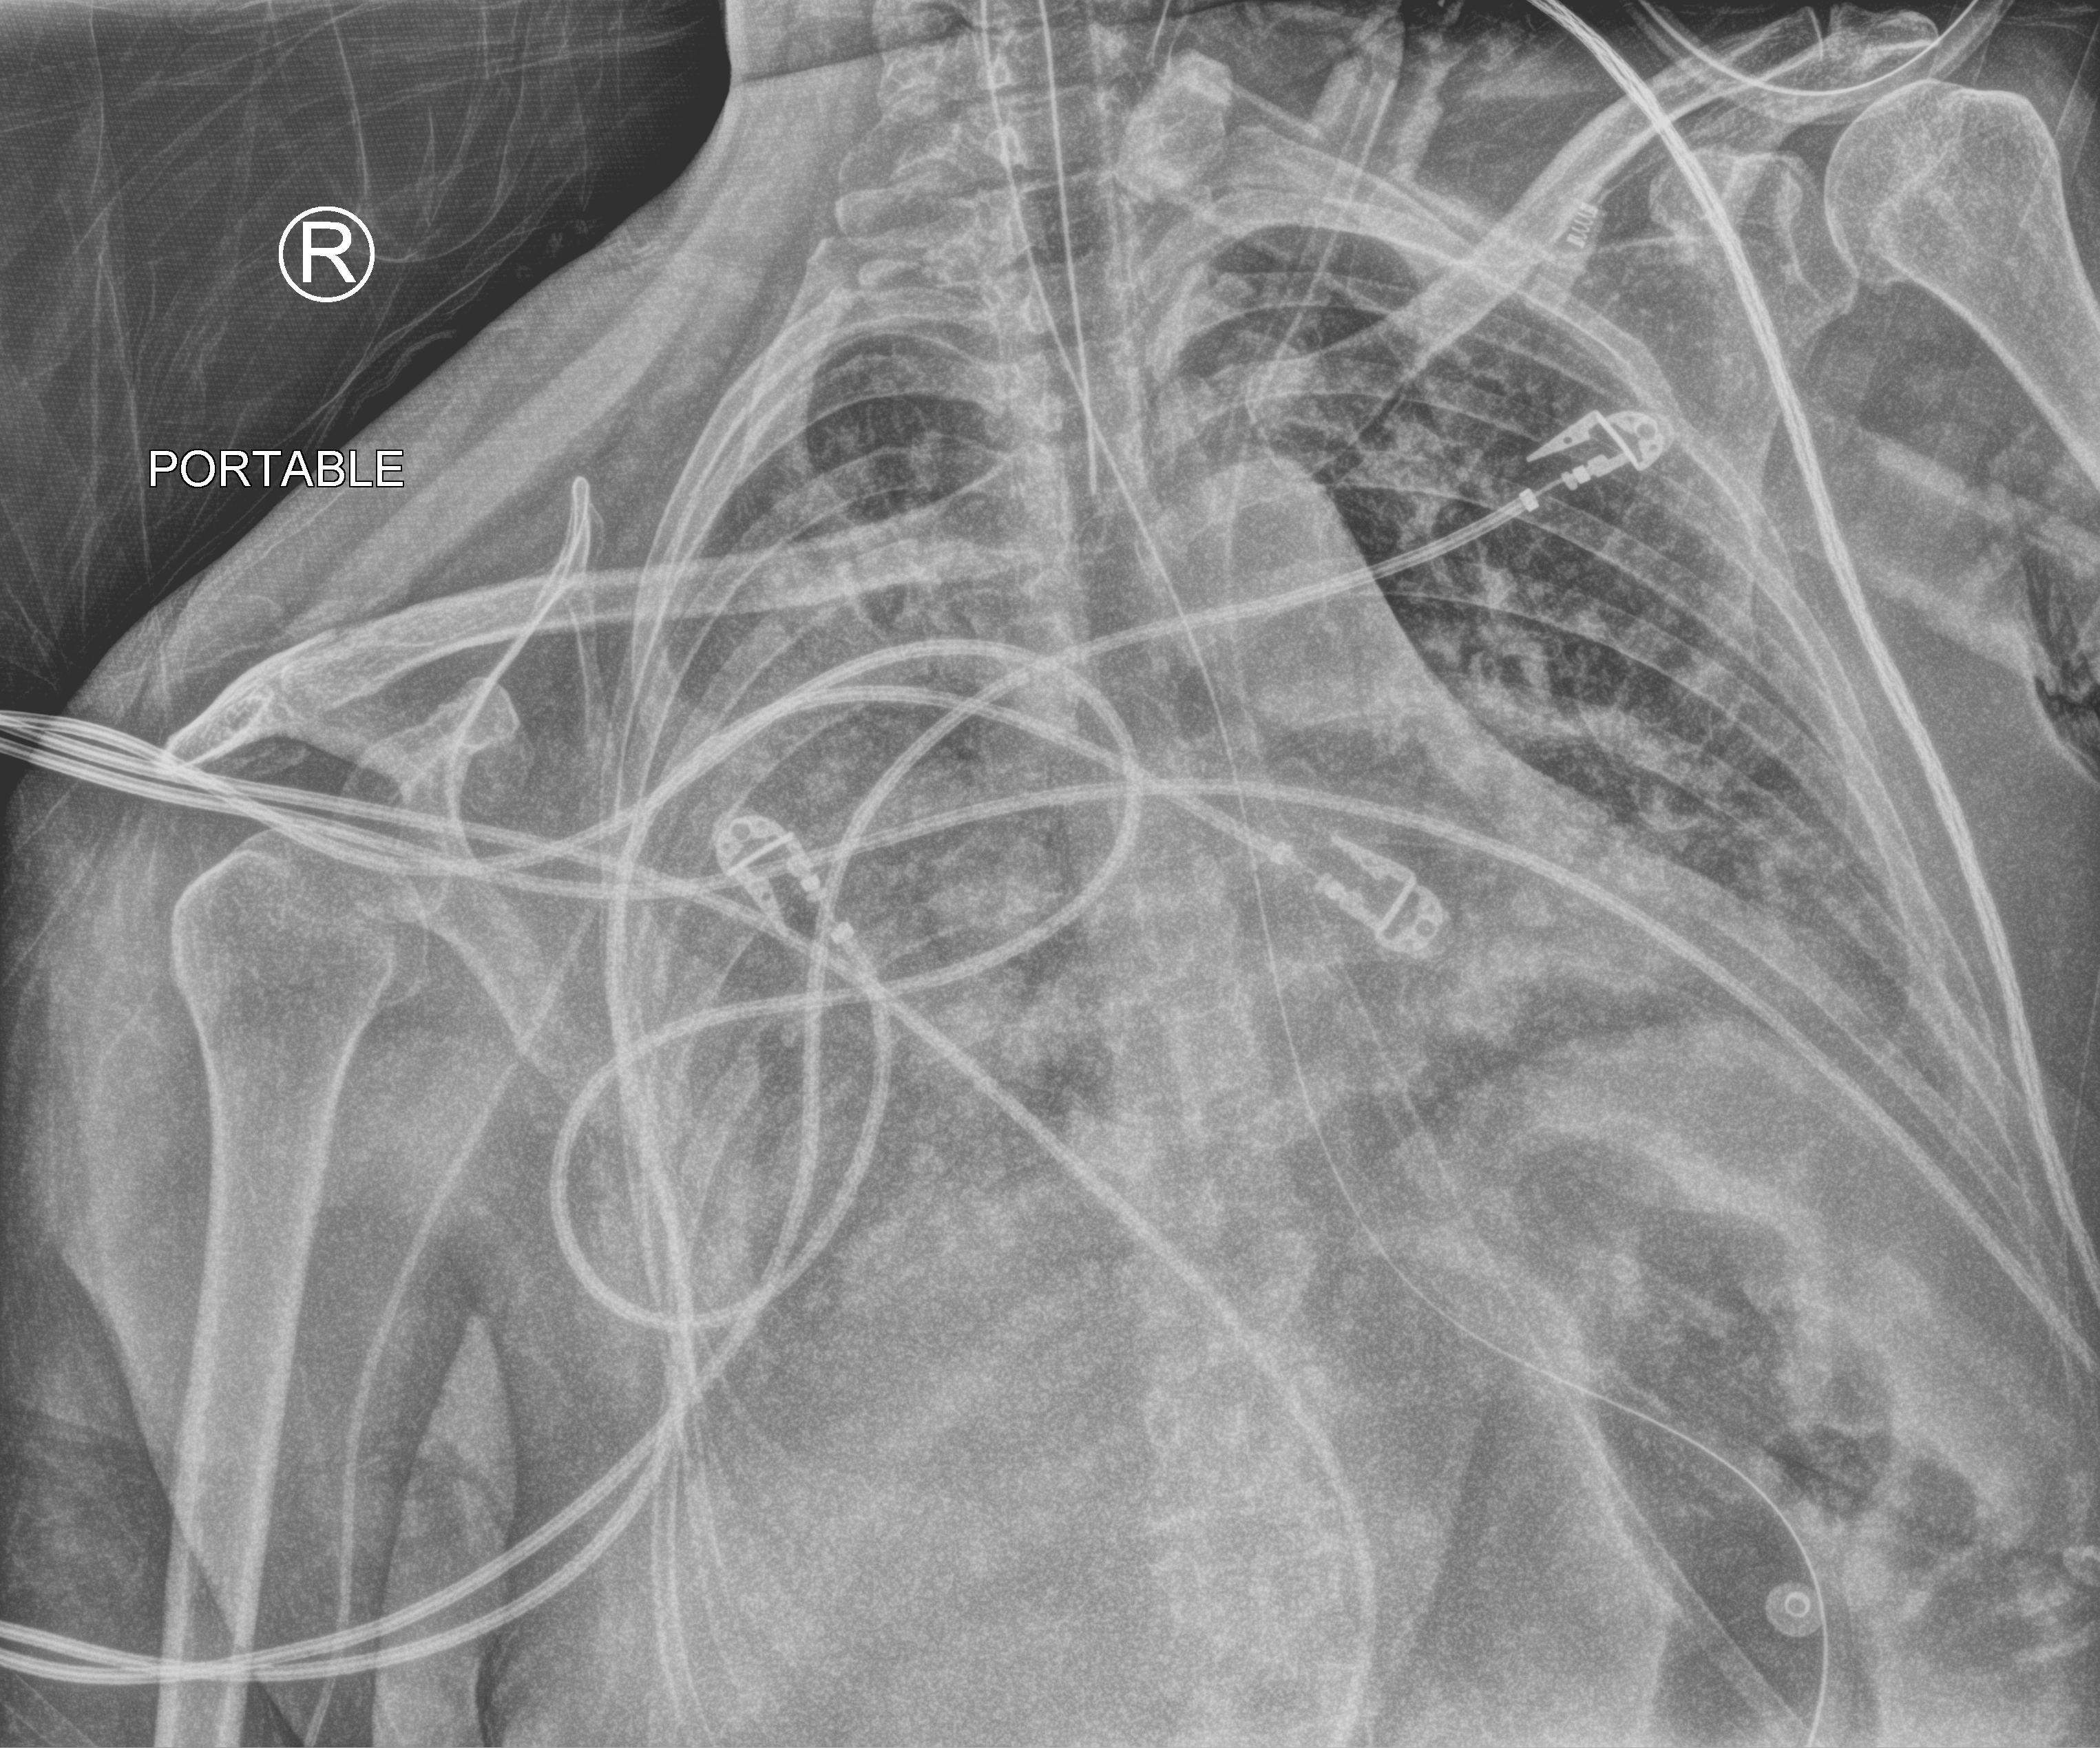
Chest X-ray (portable), anteroposterior (AP) projection. Female patient hospitalised with COVID-19, age 18–59 years.
Hospital-stay facts (about this admission, not read from this image; timing relative to this image not recorded):
- mechanically ventilated during this hospital stay: yes